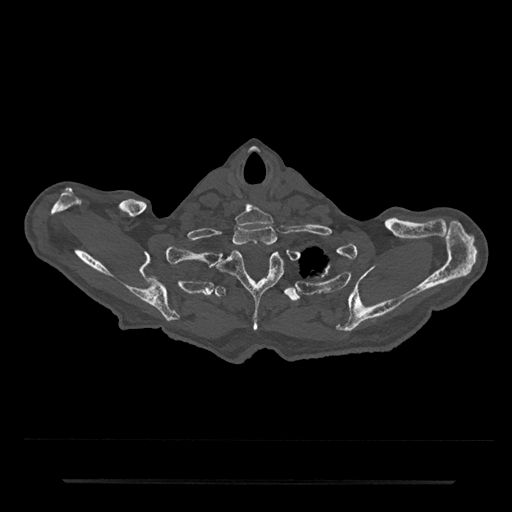
CT including the spine, one axial slice. Slice 699 of 797 in the series (ordered by position). Reconstruction kernel Br40s/3. Bone window (W 1800 / L 400 HU). 512 × 512 image matrix. Male patient, age 74 years. From the clinical record (not read from this slice): primary cancer: prostate.
Outlined on this slice (semi-automatically segmented with operator editing):
- T1 vertebra: box from (x=233, y=225) to (x=277, y=246) px
- T2 vertebra: (x=214, y=250)–(x=283, y=331)
- T3 vertebra: (x=215, y=286)–(x=300, y=302)